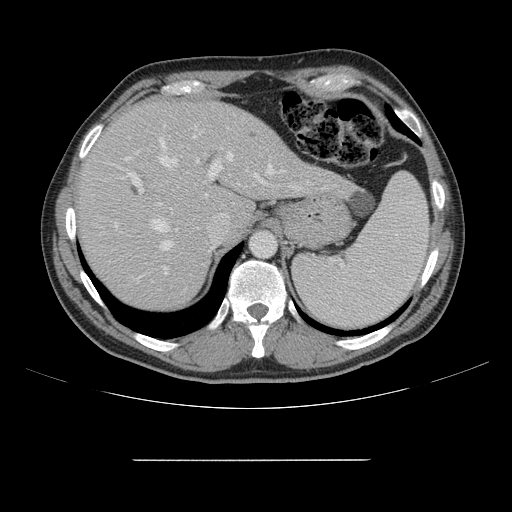
Contrast-enhanced abdominal CT, one axial slice. Position 116 of 164 along the scan axis. 120 kVp. Intravenous contrast given. Soft-tissue window (W 400 / L 40 HU). 2.5 mm slice thickness. 512 × 512 image matrix, field of view 404 × 404 mm. Male patient, age 54 years. From the clinical record (not read from this slice): diagnosis: colorectal cancer liver metastases, imaged before liver resection; multiple liver metastases: yes; largest metastasis: 1 cm; disease in both lobes: no.
Annotated regions visible in this slice (outlined manually by an expert reader):
- hepatic veins: bounding box [x1, y1, x2, y2] px = [152, 139, 285, 281]
- liver: [78, 102, 342, 308]
- planned liver remnant (the part of the liver to remain after resection): [77, 102, 248, 308]
- portal vein (with intrahepatic branches): [115, 126, 262, 284]